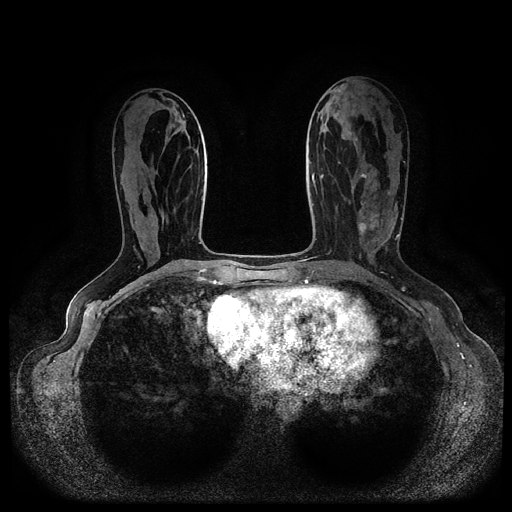
Breast MRI (dynamic contrast-enhanced, multi-phase), one axial slice. Dynamic contrast-enhanced series, time point 2 of 5 at this slice position (early post-contrast). 1.5 T. TE 2.6 ms, TR 5.3 ms. 512 × 512 image matrix, field of view 350 × 350 mm. Patient: female, 45 years.
Structures marked on this image (semi-automatically segmented with operator editing):
- breast lesion (labelled 'tumour' in the annotation; benign lesions carry a separate 'benign' label): box from (x=355, y=211) to (x=383, y=241) px